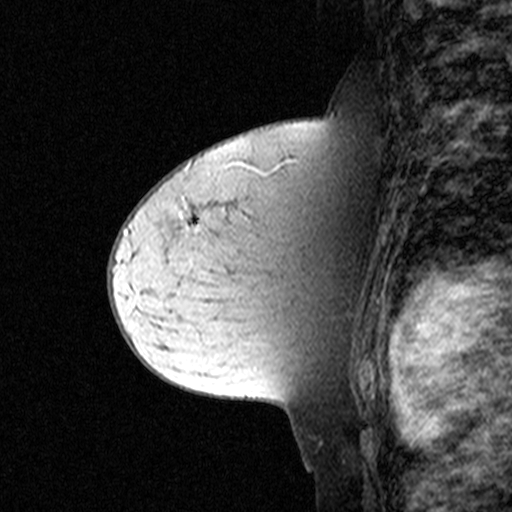
Breast MRI (dynamic contrast-enhanced), one sagittal slice; dynamic contrast-enhanced study with each time point stored as its own series, time point 2 of 3 at this slice position (early post-contrast, ordered by acquisition time); 1.5 T; TE 4.5 ms, TR 11 ms; 3 mm slice thickness; 512 × 512 image matrix, field of view 200 × 200 mm. Female patient, age 44 years. From the clinical record (not read from this slice): setting: breast cancer imaged before/during neoadjuvant chemotherapy; receptor status: triple-negative.
Structures marked on this image (semi-automatic segmentation, software-assisted and operator-edited):
- analysis volume of interest (the breast-tissue region the enhancement analysis was run in; not a lesion): box from (x=174, y=204) to (x=303, y=305) px
- tumour enhancement mask (voxels above the 90 % enhancement threshold inside the analysis volume of interest): (x=184, y=215)–(x=207, y=233)